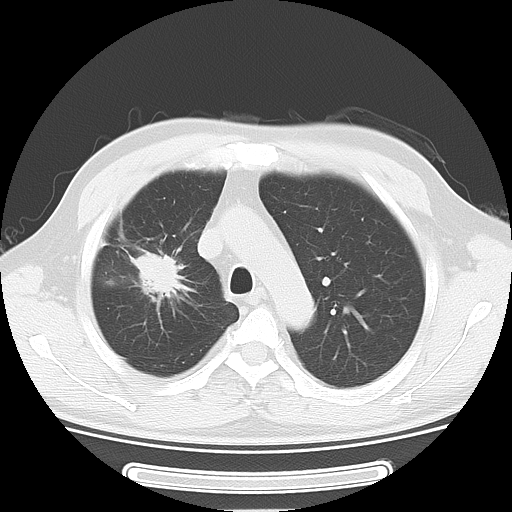
Chest CT, one axial slice. Slice 39 of 51 in the series (ordered by position). Reconstruction kernel LUNG. 120 kVp. Lung window (W 1500 / L -600 HU). 5 mm slice thickness. 512 × 512 image matrix, field of view 350 × 350 mm. Patient: male, 46 years. Case-level facts recorded for this patient, not image findings: clinical TNM (as recorded): T3 N0 M1b.
Outlined on this slice (rectangle marked by the reading radiologist):
- lung tumour (recorded histology: adenocarcinoma): bounding box [x1, y1, x2, y2] px = [124, 244, 177, 300]